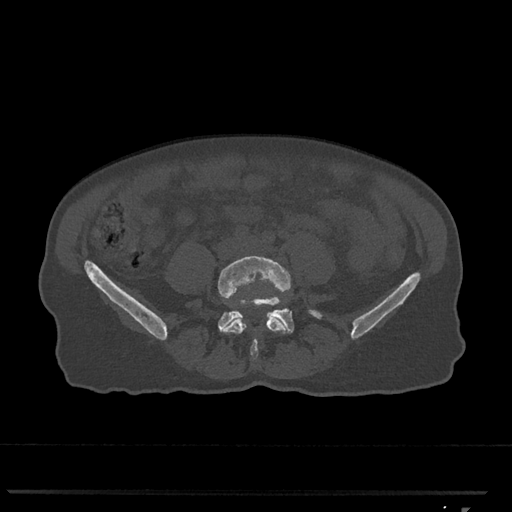
CT including the spine, one axial slice; slice 181 of 793 in the series (ordered by position); reconstruction kernel Br40s/3; 120 kVp; bone window (W 1800 / L 400 HU); 512 × 512 image matrix, field of view 380 × 380 mm. Patient: female, 62 years. From the clinical record (not read from this slice): primary cancer: renal.
Structures marked on this image (semi-automatically segmented with operator editing):
- L4 vertebra: bounding box [x1, y1, x2, y2] px = [218, 255, 291, 359]
- L5 vertebra: [218, 297, 322, 333]